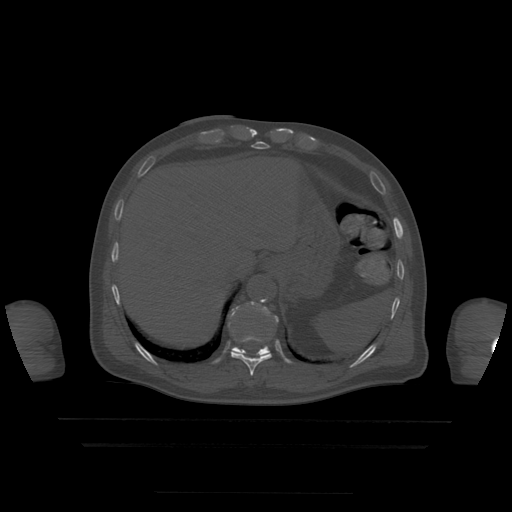
CT including the spine, one axial slice; slice 233 of 522 in the series (ordered by position); bone window (W 1800 / L 400 HU); 512 × 512 image matrix. Patient age 68 years. From the clinical record (not read from this slice): primary cancer: urothelial.
Structures marked on this image (semi-automatically segmented with operator editing):
- T10 vertebra: bounding box [x1, y1, x2, y2] px = [229, 309, 272, 376]
- T11 vertebra: [232, 302, 279, 357]